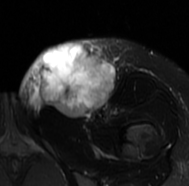
MRI of an extremity soft-tissue mass, one axial slice. Slice 35 of 77 in the series (ordered by position). T2-weighted fat-saturated. MR volume resampled by the dataset authors to the PET/CT grid (not the native acquisition matrix). 189 × 186 image matrix. Female patient. From the clinical record (not read from this slice): histological type: leiomyosarcoma; grade: high; site of the primary tumour: groin.
Outlined on this slice (expert contour drawn on MRI and transferred to this co-registered scan by the dataset authors):
- gross tumour volume including surrounding oedema: box from (x=17, y=38) to (x=130, y=117) px
- gross tumour volume (mass): (x=35, y=43)–(x=114, y=117)